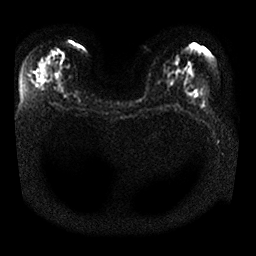
Breast MRI, one axial slice; slice 17 of 25 in the series (ordered by position); diffusion-weighted series; image 2 of 4 stored at this slice position (different b-values; order by instance number); 1.5 T; 4 mm slice thickness; 256 × 256 image matrix. Female patient.
Structures marked on this image (outlined manually by an expert reader):
- tumour on diffusion-weighted imaging: bounding box [x1, y1, x2, y2] px = [51, 48, 67, 62]